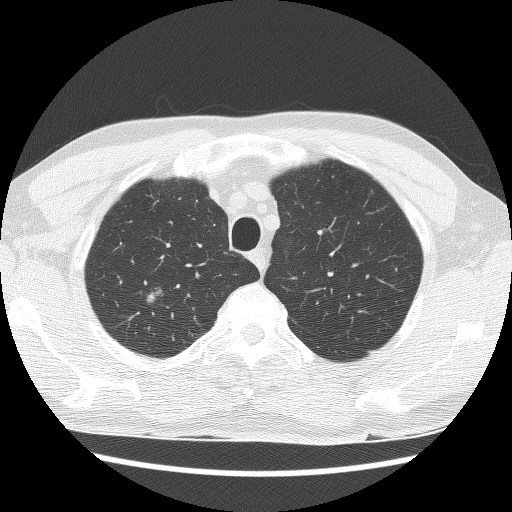
Axial slice from a low-dose chest CT screening exam. Second screening round (one year after baseline). Lung window (W 1500 / L -600 HU). Lung (sharp) reconstruction kernel (BONE). Male, age 66 years at enrolment.
Expert reader's lesion annotation, bounding box [x1, y1, x2, y2] px = [138, 283, 172, 310]. The exam's reader record, not a measurement of the box and not confirmed to be the same lesion: non-calcified nodule or mass ≥4 mm, right upper lobe, 7 × 6 mm, poorly defined margins, mixed attenuation, pre-existing on the prior screen: yes; interval growth: yes. Official screen result: positive, other. Lung cancer was diagnosed 277 days after this screen: squamous cell carcinoma, NOS, right upper lobe, moderately differentiated (G2), stage IIB (AJCC 6th edition), 39 mm at pathology.